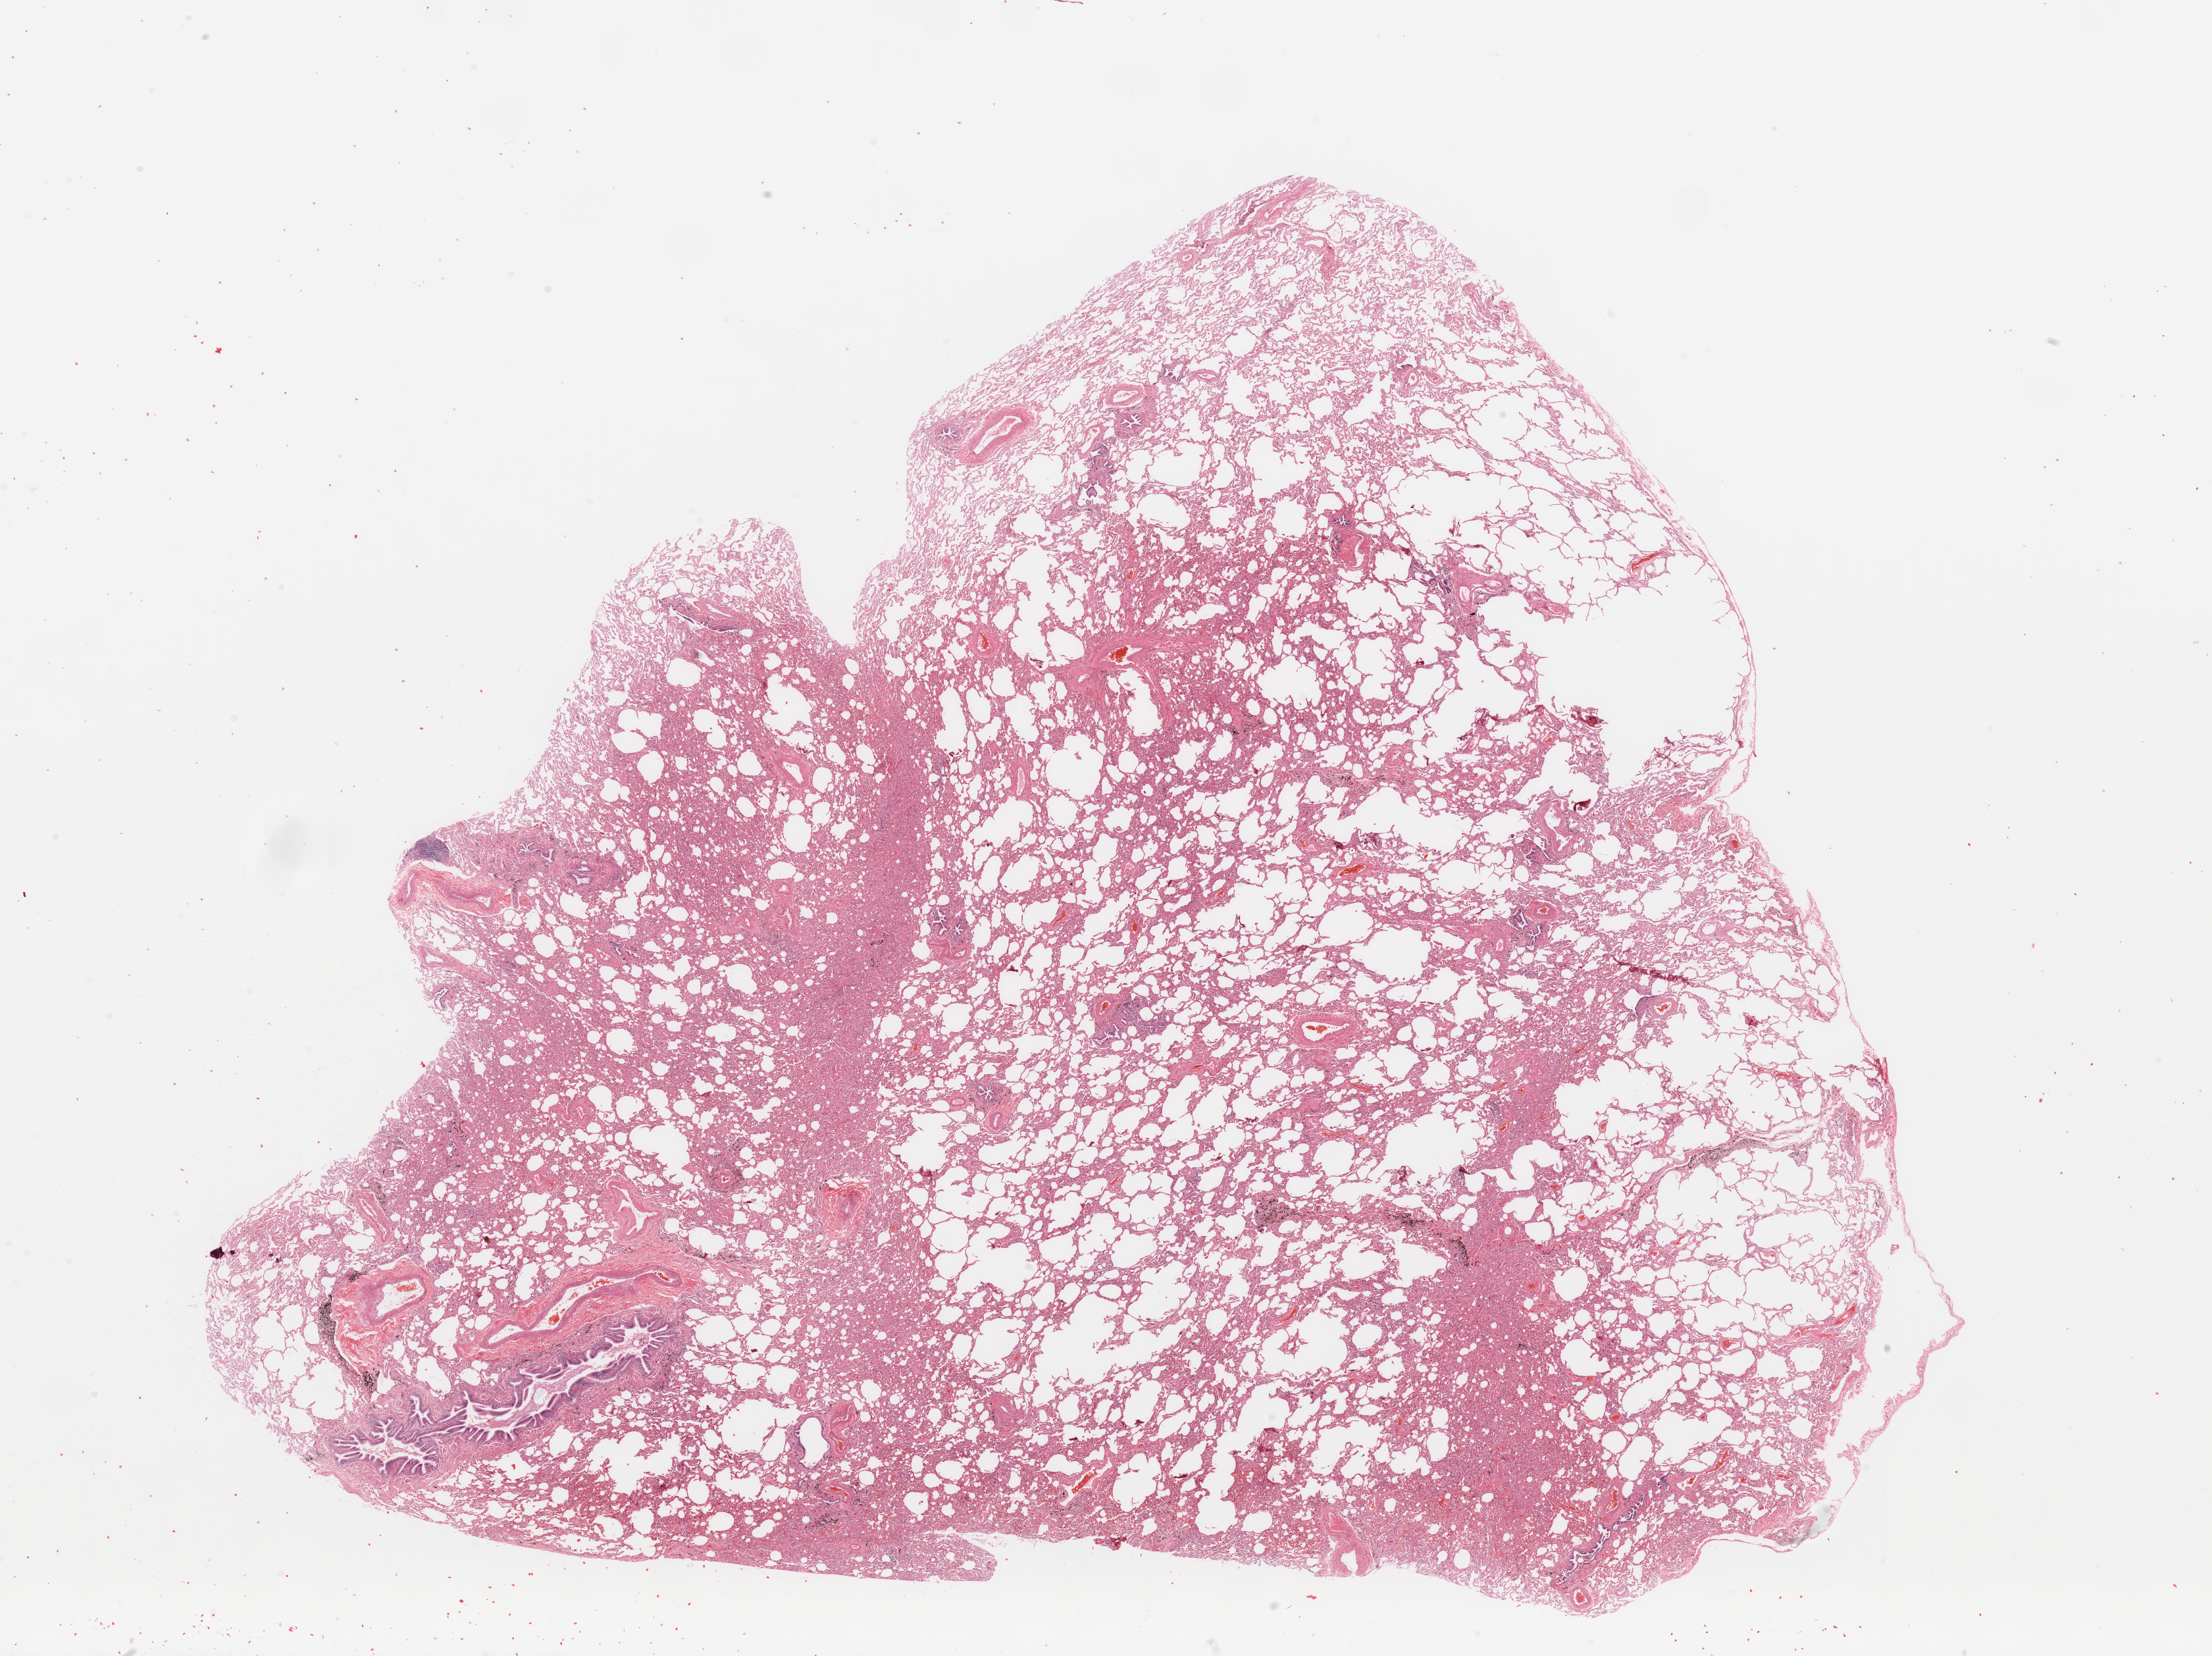
Digitized H&E tissue section (whole slide) — a low-resolution overview of the entire scanned area, about 26.6 x 19.9 mm (acquisition: 20x scan); normal (non-tumour) tissue sample, sampled site: lung. Female, 68 y/o.
* this section: normal (non-tumour) tissue from the same patient
* patient diagnosis: Adenocarcinoma, NOS